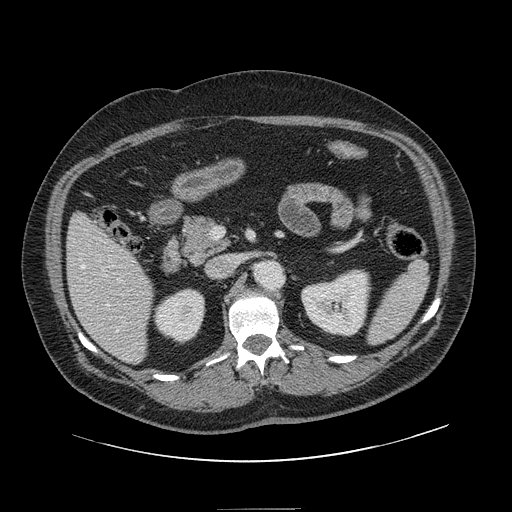
Contrast-enhanced abdominal CT, one axial slice; position 64 of 154 along the scan axis; intravenous contrast given; soft-tissue window (W 400 / L 40 HU); 2.5 mm slice thickness; 512 × 512 image matrix, field of view 451 × 451 mm. Male patient, age 61 years. Case-level facts recorded for this patient, not image findings: diagnosis: colorectal cancer liver metastases, imaged before liver resection; multiple liver metastases: yes; largest metastasis: 2.6 cm.
Structures marked on this image (expert manual segmentation):
- hepatic veins: bounding box [x1, y1, x2, y2] px = [81, 265, 119, 332]
- liver: [68, 215, 153, 363]
- planned liver remnant (the part of the liver to remain after resection): [68, 214, 153, 363]